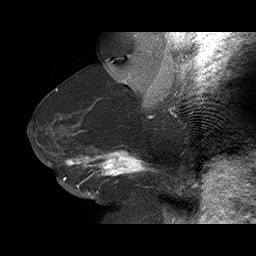
Breast MRI (dynamic contrast-enhanced), one sagittal slice. Slice 40 of 75 in the series (ordered by position). Dynamic contrast-enhanced series, time point 2 of 6 at this slice position (early post-contrast). 1.5 T. TE 4.5 ms, TR 32.4 ms. 3 mm slice thickness. 256 × 256 image matrix, field of view 180 × 180 mm. Female patient. Case-level facts recorded for this patient, not image findings: setting: breast cancer imaged before/during neoadjuvant chemotherapy; receptor status: HR-positive, HER2-negative.
Outlined on this slice (semi-automatically segmented with operator editing):
- analysis volume of interest (the breast-tissue region the enhancement analysis was run in; not a lesion): box from (x=58, y=134) to (x=166, y=191) px
- tumour enhancement mask (voxels above the 100 % enhancement threshold inside the analysis volume of interest): (x=63, y=134)–(x=151, y=188)